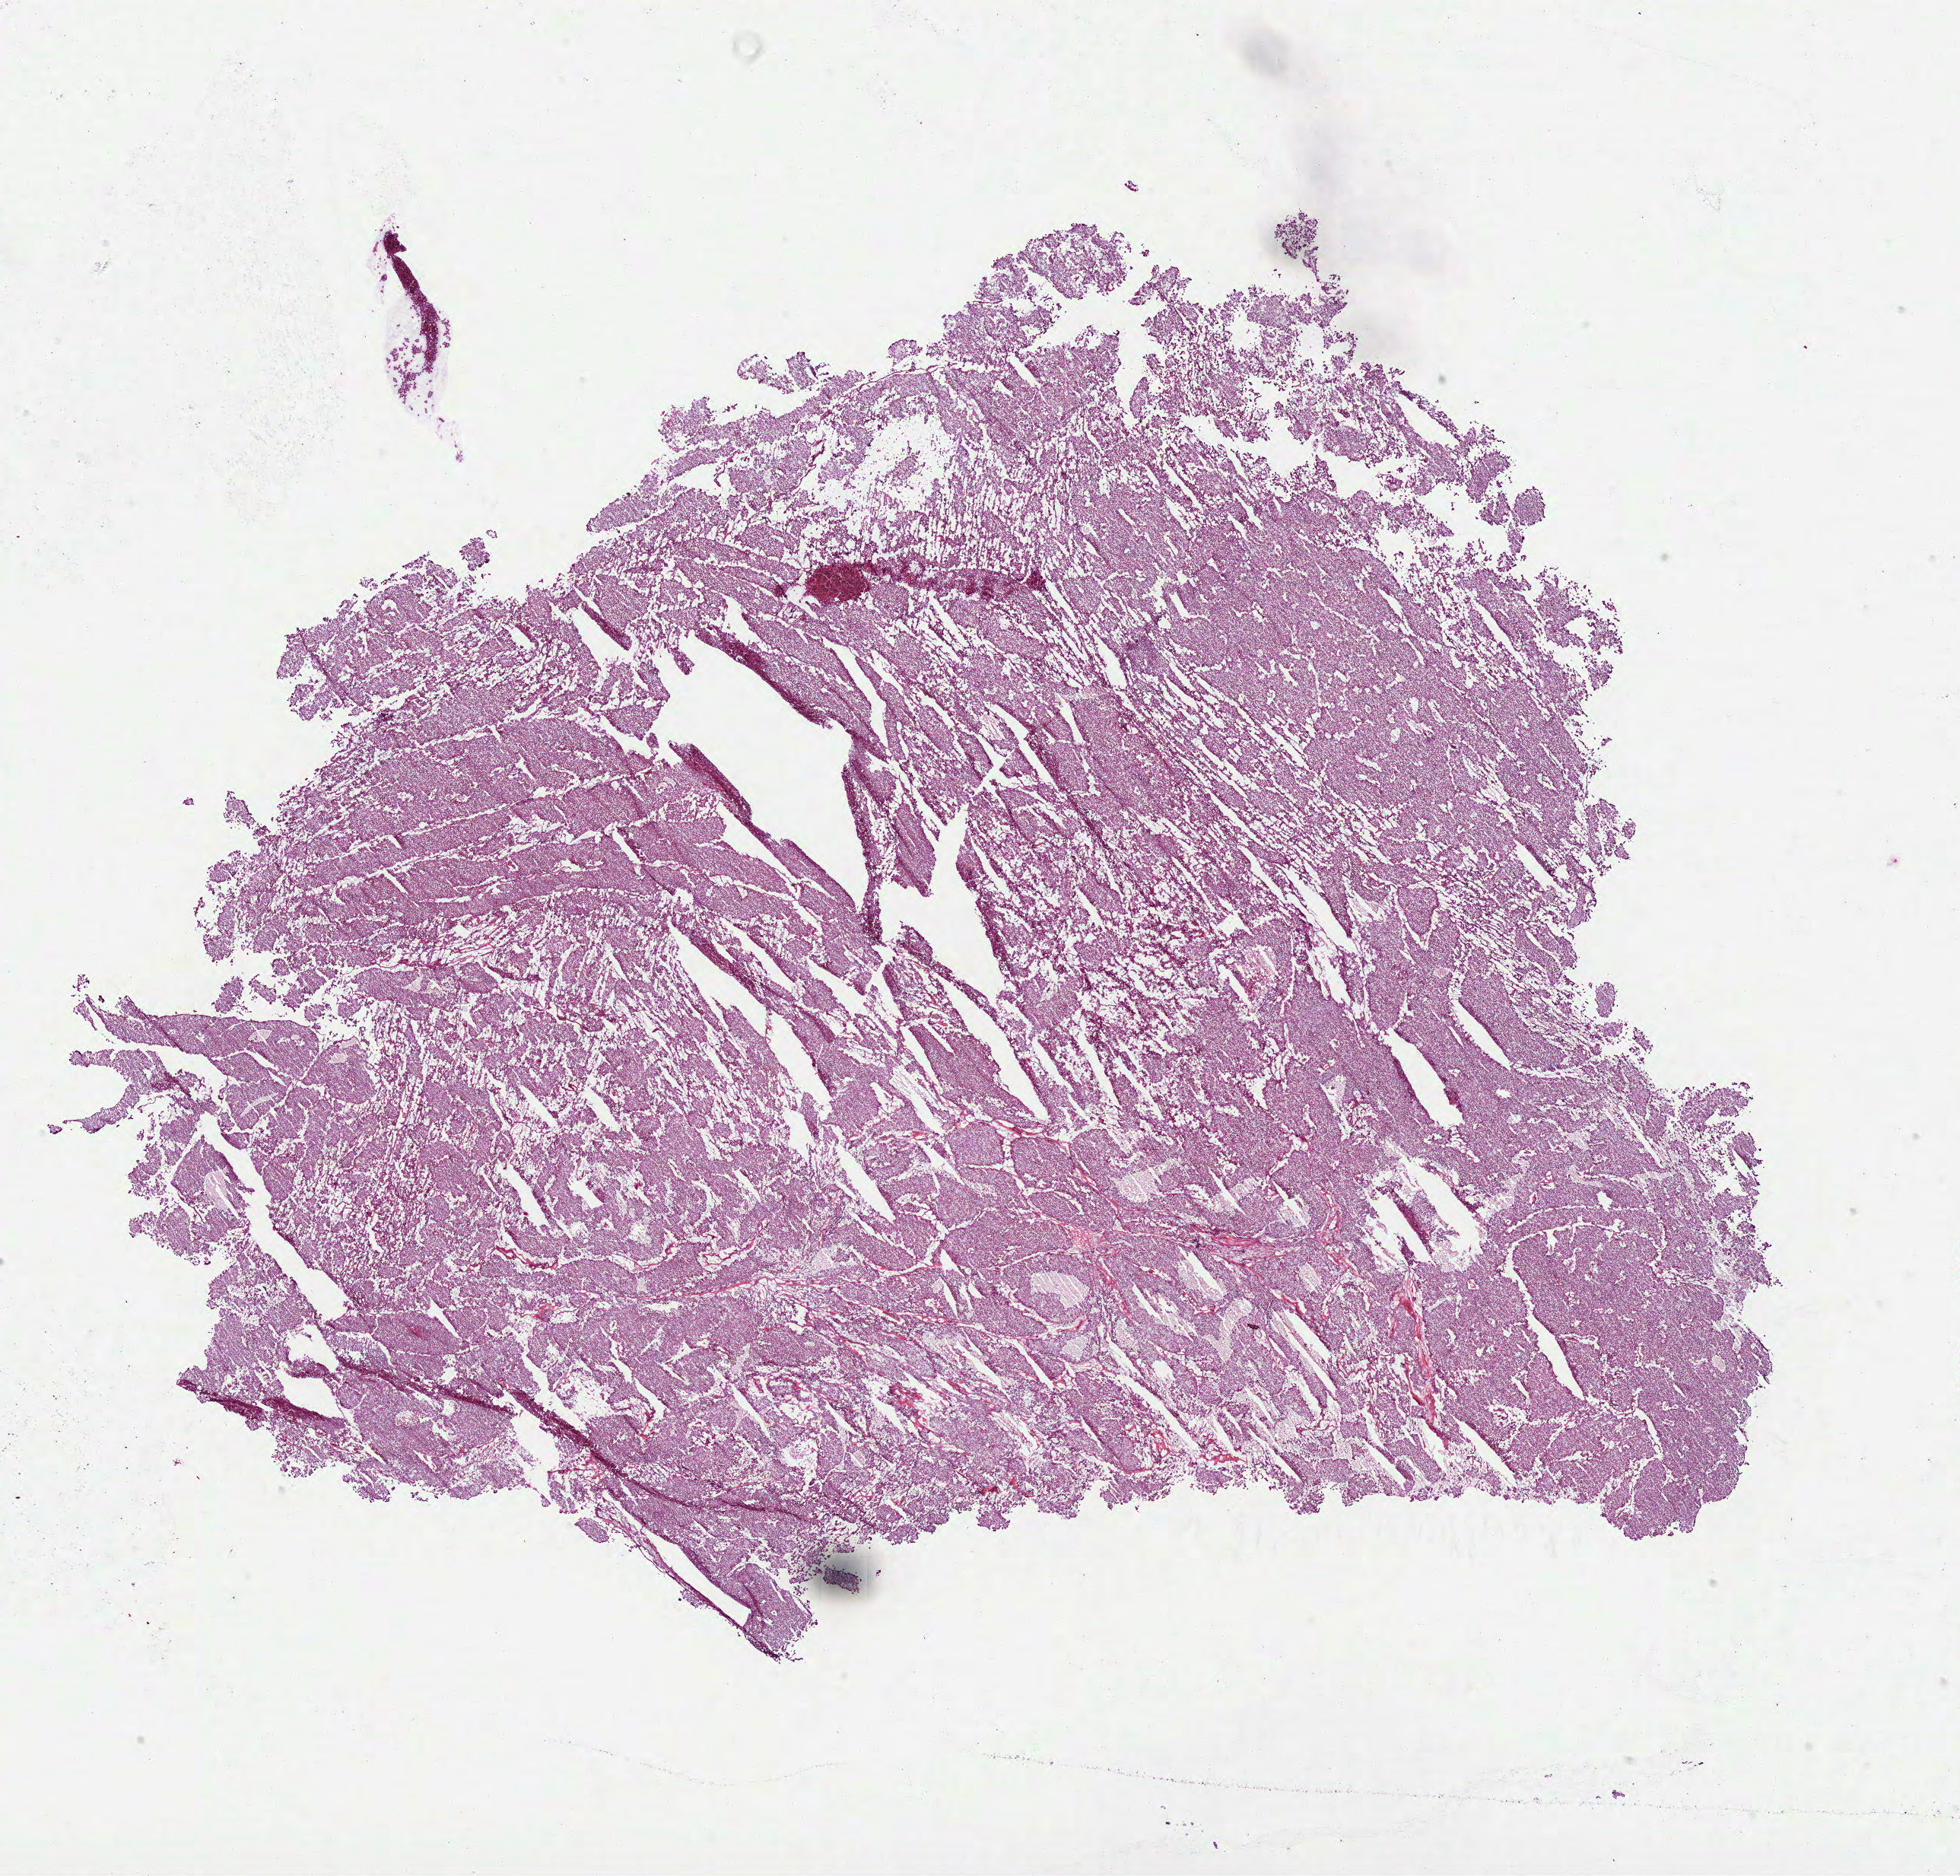
Digitized H&E-stained tissue section (whole slide), shown as a low-resolution overview of the whole scanned area (about 20.8 x 19.9 mm), frozen section, sample: primary tumour, kidney. Male, age 59 years at initial diagnosis. Pathologist review of this section (percent, as recorded): tumour cells 100%, tumour nuclei 95%, normal cells 0%, stromal cells 0%, necrosis 0%. Infiltration values recorded for this section: lymphocyte infiltration 0%, monocyte infiltration 0%, neutrophil infiltration 0%.
• TNM: T2 NX
• AJCC pathologic stage: II (6th edition)
• histologic diagnosis: Renal cell carcinoma, chromophobe type